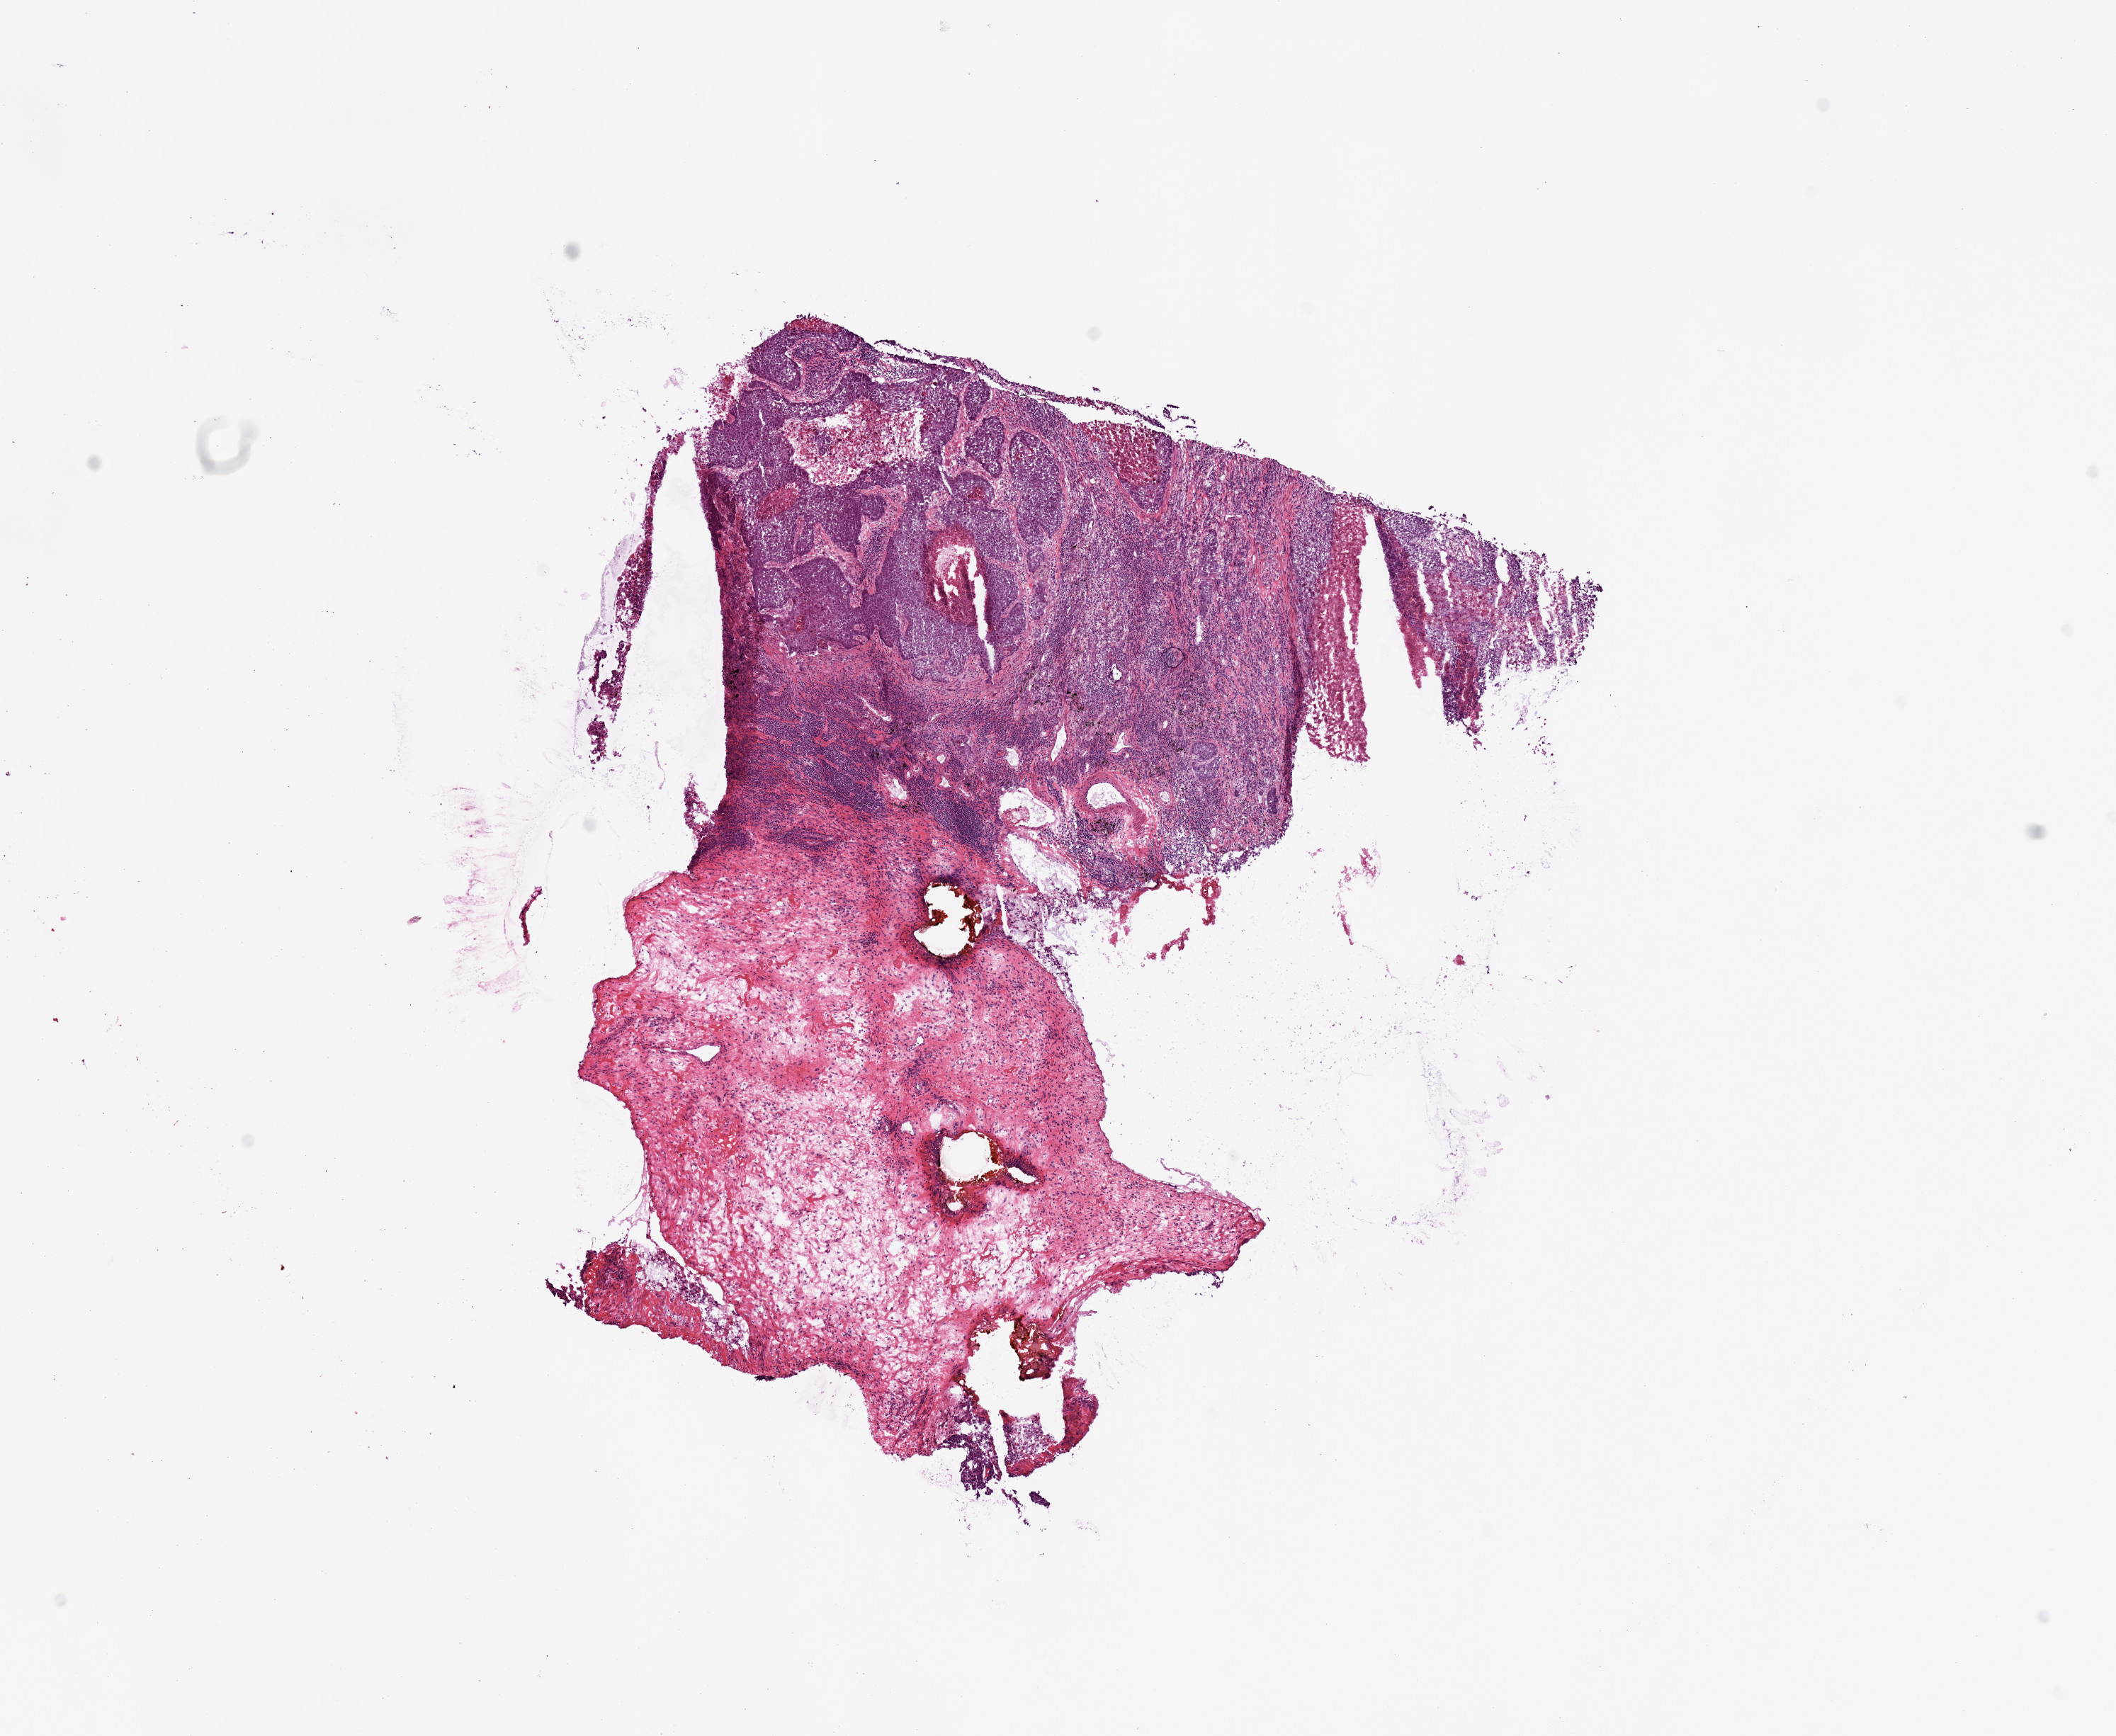
Whole-slide histology image, H&E — shown as a low-resolution overview of the whole scanned area (about 11.8 x 9.7 mm), frozen section, lung, primary tumour sample. Male, age 76 years at initial diagnosis. Slide review estimates, as recorded: tumour cells 85%, tumour nuclei 60%, normal cells 0%, stromal cells 15%, necrosis 0%.
• AJCC pathologic stage: IIB (6th edition)
• TNM: T2 N1 MX
• diagnosis: Squamous cell carcinoma, NOS (middle lobe, lung)